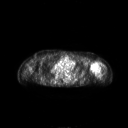
FDG PET of an extremity soft-tissue mass (from a PET/CT study), one axial slice. Slice 177 of 267 in the series (ordered by position). 3.27 mm slice thickness. 128 × 128 image matrix. Female patient, age 83 years. Case-level facts recorded for this patient, not image findings: histological type: pleiomorphic leiomyosarcoma; grade: high; site of the primary tumour: left biceps.
Outlined on this slice (expert contour drawn on MRI and transferred to this co-registered scan by the dataset authors):
- gross tumour volume including surrounding oedema: bounding box (x1, y1, x2, y2) in pixels: (90, 61, 102, 77)
- gross tumour volume (mass): (90, 61, 101, 74)